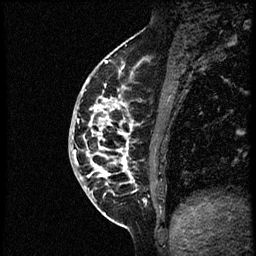
Breast MRI (dynamic contrast-enhanced), one sagittal slice; slice 22 of 56 in the series (ordered by position); dynamic contrast-enhanced study with each time point stored as its own series, time point 2 of 3 at this slice position (early post-contrast, ordered by acquisition time); 1.5 T; TE 4.2 ms, TR 21.3 ms; 2 mm slice thickness; 256 × 256 image matrix. Patient: female, 41 years. Case-level facts recorded for this patient, not image findings: setting: breast cancer imaged before/during neoadjuvant chemotherapy; receptor status: HER2-positive.
Outlined on this slice (semi-automatically segmented with operator editing):
- analysis volume of interest (the breast-tissue region the enhancement analysis was run in; not a lesion): bounding box (x1, y1, x2, y2) in pixels: (70, 73, 175, 205)
- tumour enhancement mask (voxels above the 100 % enhancement threshold inside the analysis volume of interest): (72, 78, 134, 181)